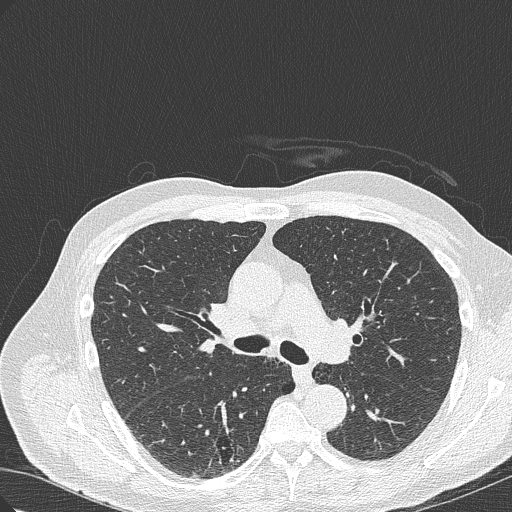
Axial slice from a low-dose chest CT screening exam, baseline annual screen, lung window (W 1500 / L -600 HU), 120 kVp, slice 120 of 322 in the series. Male participant, aged 70 years at enrolment. Current smoker at enrolment.
Lesion marked by an expert reader, box from (x=200, y=419) to (x=264, y=470) px. The screening reader recorded 4 non-calcified nodules or masses ≥4 mm on this exam; which of them this box marks is not recorded. Official screen result: positive, change unspecified: nodule(s) >= 4 mm or enlarging nodule(s), mass(es), or other non-specific abnormalities suspicious for lung cancer. Participant outcome: lung cancer diagnosed 978 days after this screen (after the third annual screen) — bronchiolo-alveolar adenocarcinoma, NOS, right lower lobe, poorly differentiated (G3), stage IB (AJCC 6th edition), 30 mm at pathology.